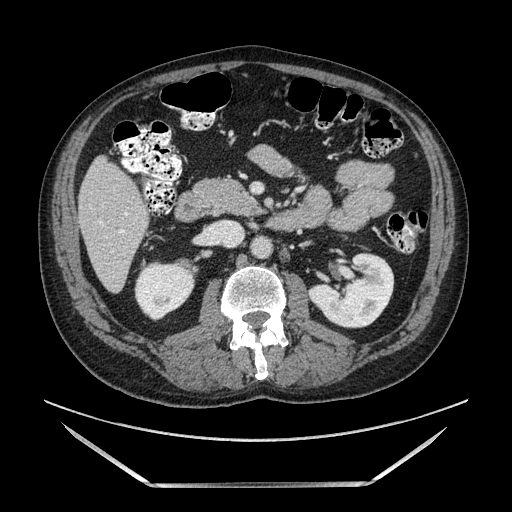
Contrast-enhanced abdominal CT, one axial slice; position 48 of 185 along the scan axis; soft-tissue window (W 400 / L 40 HU); 1.25 mm slice thickness; 512 × 512 image matrix, field of view 440 × 440 mm. Male patient. From the clinical record (not read from this slice): diagnosis: adrenocortical carcinoma; tumour side: right adrenal; tumour size at pathology: 10.3 cm; Ki-67 index: 20 %; stage (as recorded): 3.
Outlined on this slice (semi-automatically segmented with operator editing):
- mass: bounding box <178,262,193,270> (left, top, right, bottom; pixels)